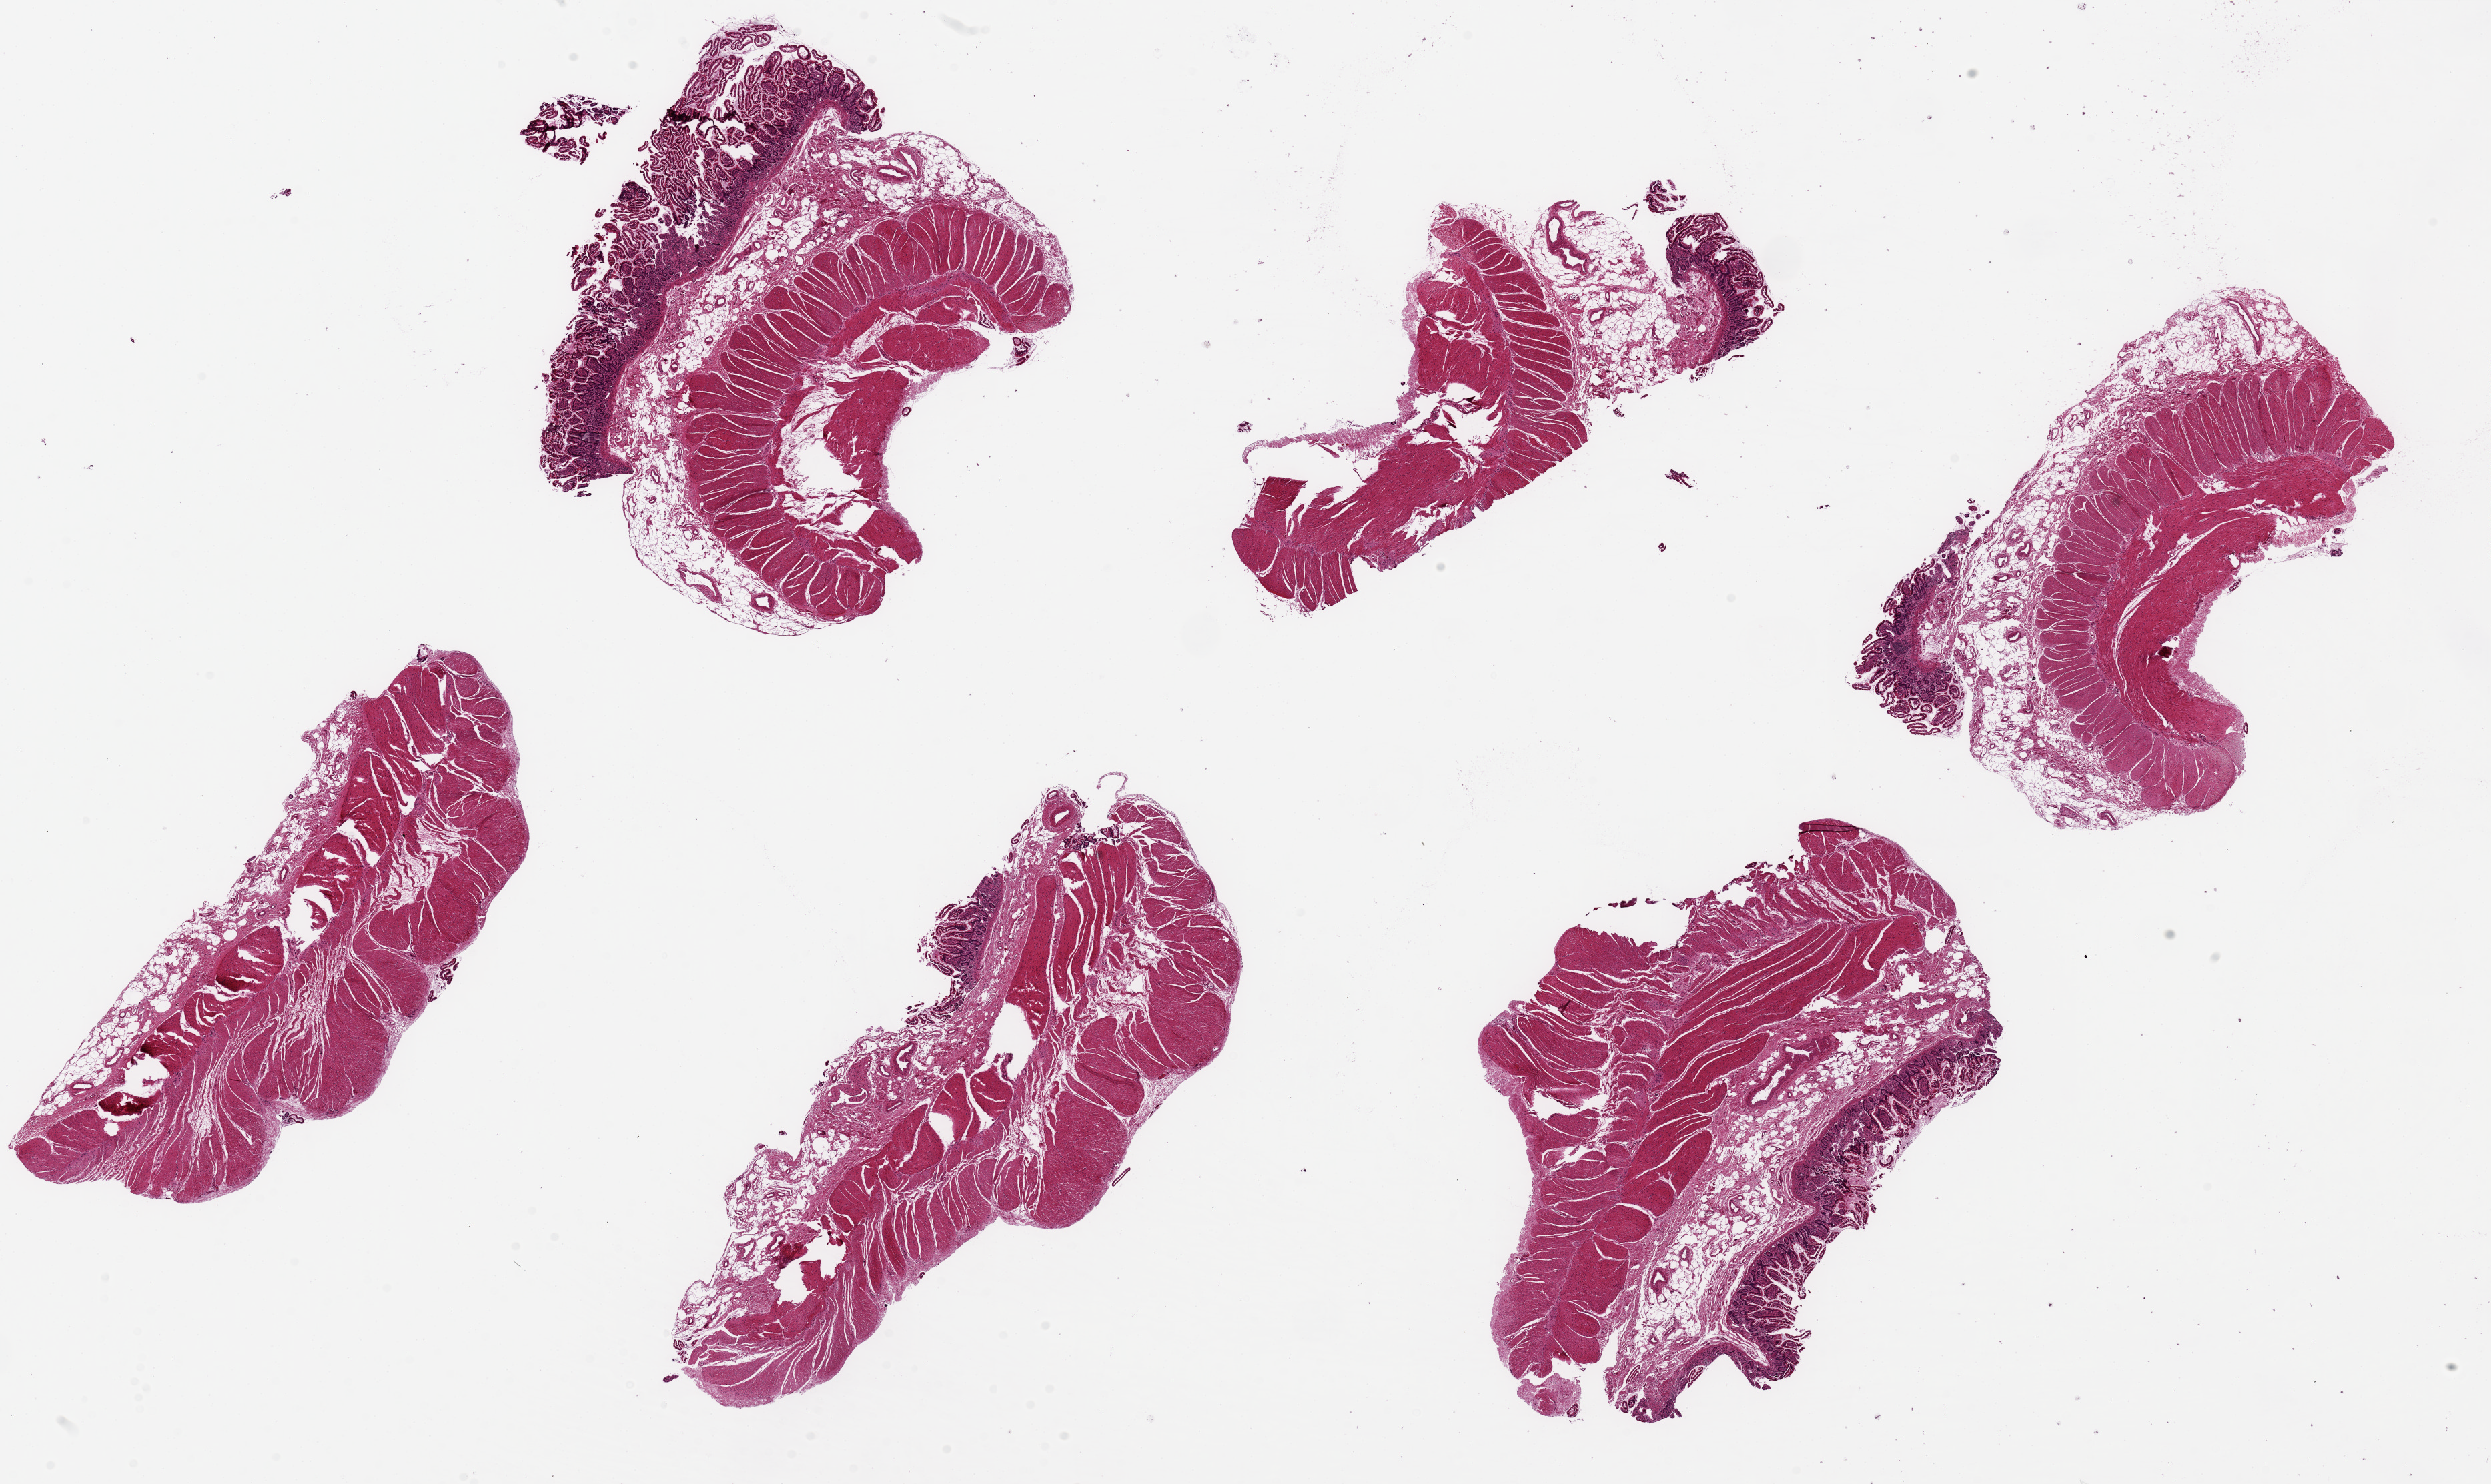
Hematoxylin and eosin (H&E) whole-slide image — shown as a low-resolution overview of the whole scanned area (about 29.5 x 17.6 mm), PAXgene-fixed paraffin-embedded (PFPE) section, section of ileum (target tissue), tissue donor sample. Donor sex: male.
Review note (as recorded): 6 pieces, up to 9x4mm; all pieces contain mostly muscle; 5 have mucosa and one small lymphoid nodule.